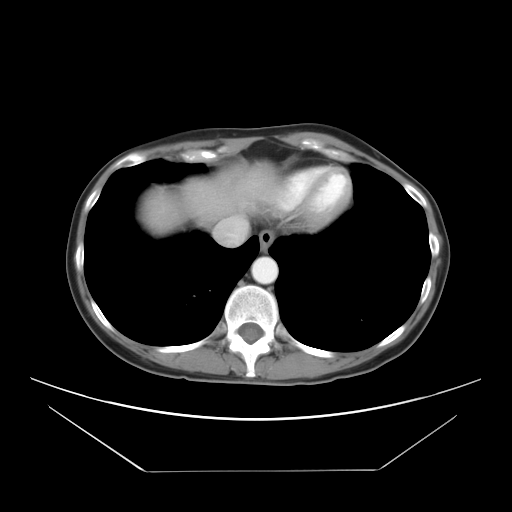
Contrast-enhanced abdominal CT, one axial slice; position 27 of 30 along the scan axis; reconstruction kernel STANDARD; intravenous contrast given; soft-tissue window (W 400 / L 40 HU); 512 × 512 image matrix. Female patient, age 54 years. From the clinical record (not read from this slice): diagnosis: colorectal cancer liver metastases, imaged before liver resection; multiple liver metastases: yes; largest metastasis: 2.5 cm; disease in both lobes: yes.
Structures marked on this image (manually delineated by an expert):
- liver: bounding box (x1, y1, x2, y2) in pixels: (184, 169, 271, 222)
- planned liver remnant (the part of the liver to remain after resection): (183, 179, 259, 222)